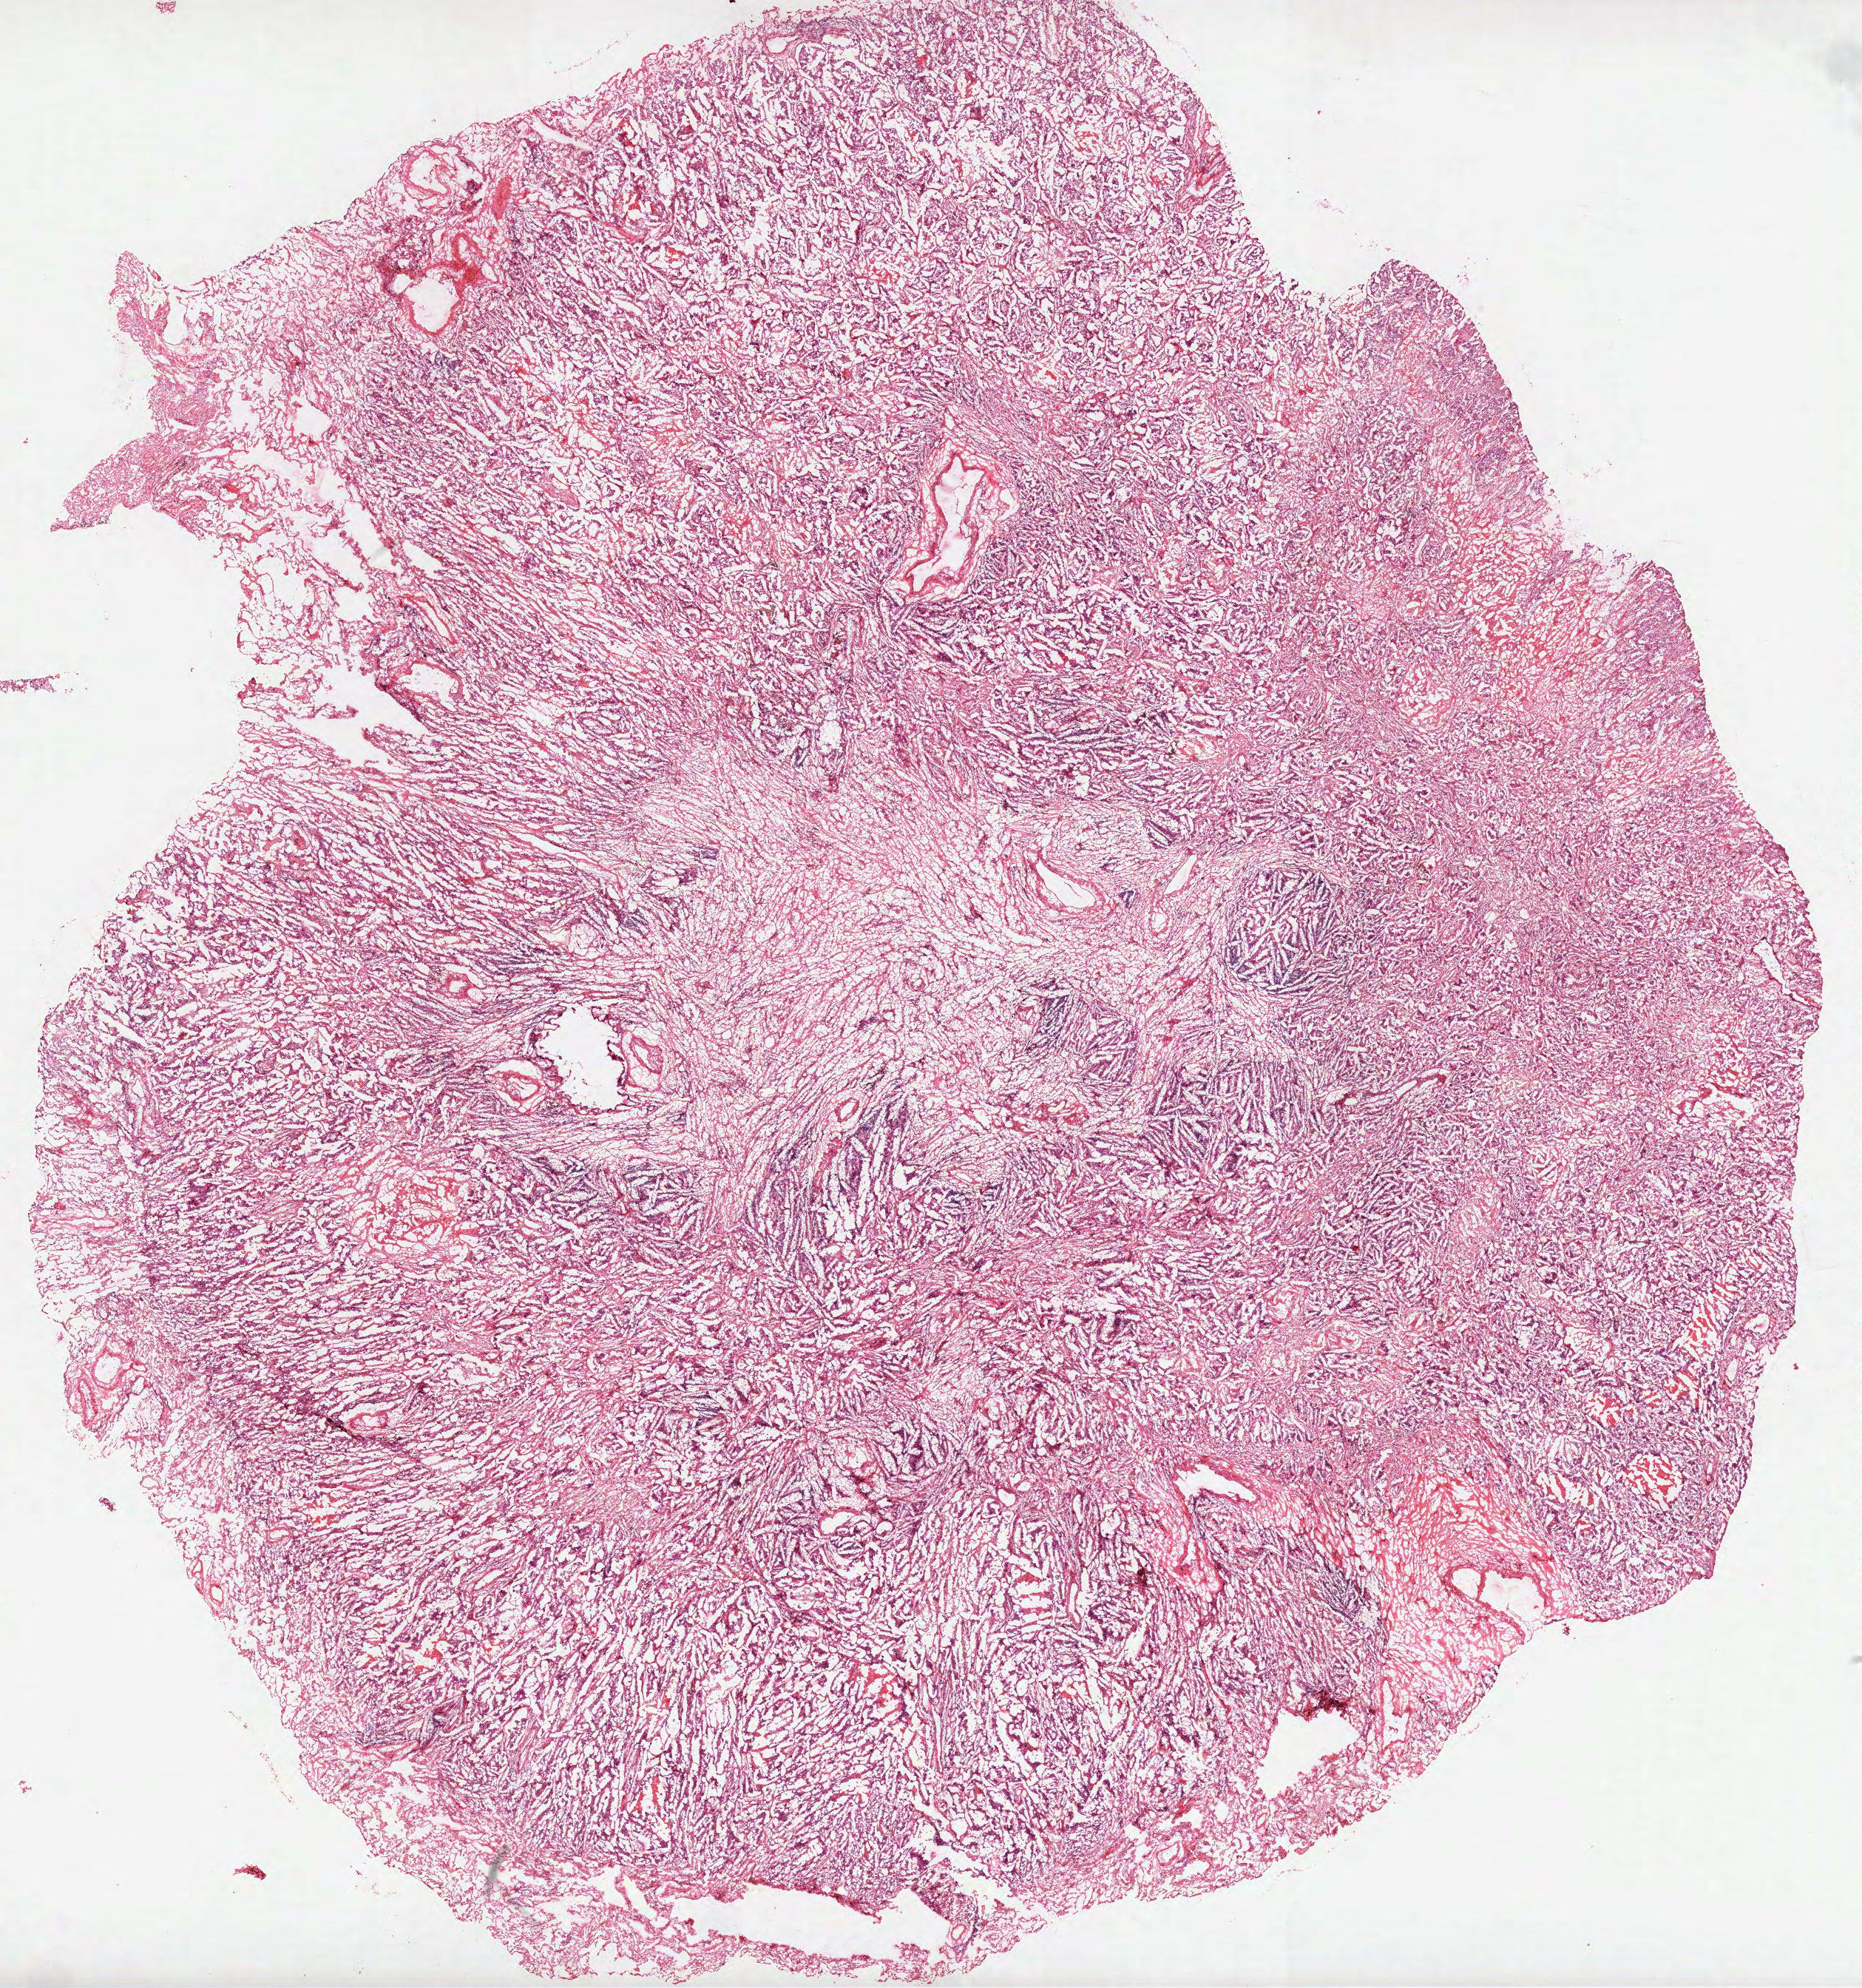
Digitized Hematoxylin and eosin (H&E) stained tissue section (whole slide), low-resolution overview of the scanned area, about 20.3 x 21.7 mm (slide scanned at 40x). Frozen section from the top of the tissue portion. Primary tumour sample from the lung. Male patient; age at initial diagnosis 57 years. Pathologist review of this section (percent, as recorded): tumour cells 80%, tumour nuclei 75%.
Histologic diagnosis: Solid carcinoma, NOS.